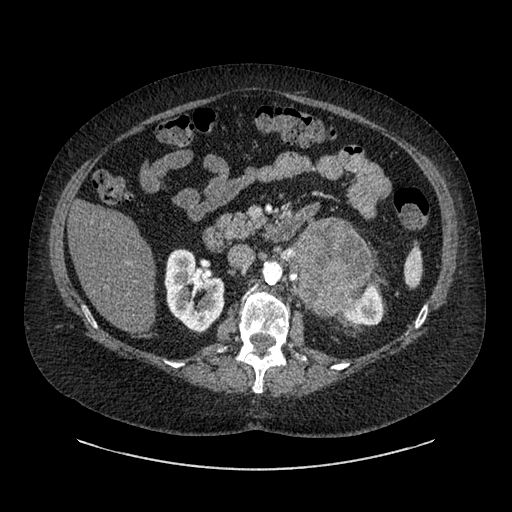
Contrast-enhanced abdominal CT, one axial slice. Position 524 of 769 along the scan axis. 120 kVp. Intravenous contrast given. Soft-tissue window (W 400 / L 40 HU). 0.62 mm slice thickness. 512 × 512 image matrix, field of view 460 × 460 mm. Female patient, age 61 years. From the clinical record (not read from this slice): diagnosis: adrenocortical carcinoma; tumour side: left adrenal; tumour size at pathology: 13 cm; Ki-67 index: 79 %; stage (as recorded): 2.
Annotated regions visible in this slice (semi-automatically segmented with operator editing):
- mass: bounding box (x1, y1, x2, y2) in pixels: (292, 220, 374, 307)